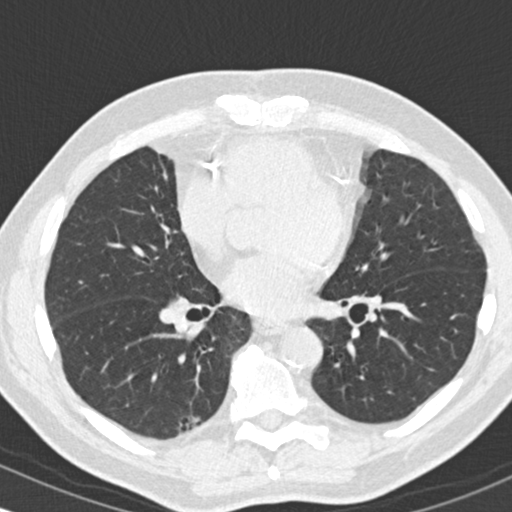
Axial slice from a low-dose chest CT screening exam. Second annual screen. Lung window (W 1500 / L -600 HU). Standard (soft-tissue) reconstruction kernel (B30f). Slice 99 of 180 in the series. Male participant, aged 68 years at enrolment. Former smoker at enrolment.
Expert-annotated lung lesion, bounding box <164,405,220,446> (left, top, right, bottom; pixels). The screening reader recorded 2 non-calcified nodules or masses ≥4 mm on this exam (lingula, right upper lobe); which of them this box marks is not recorded.